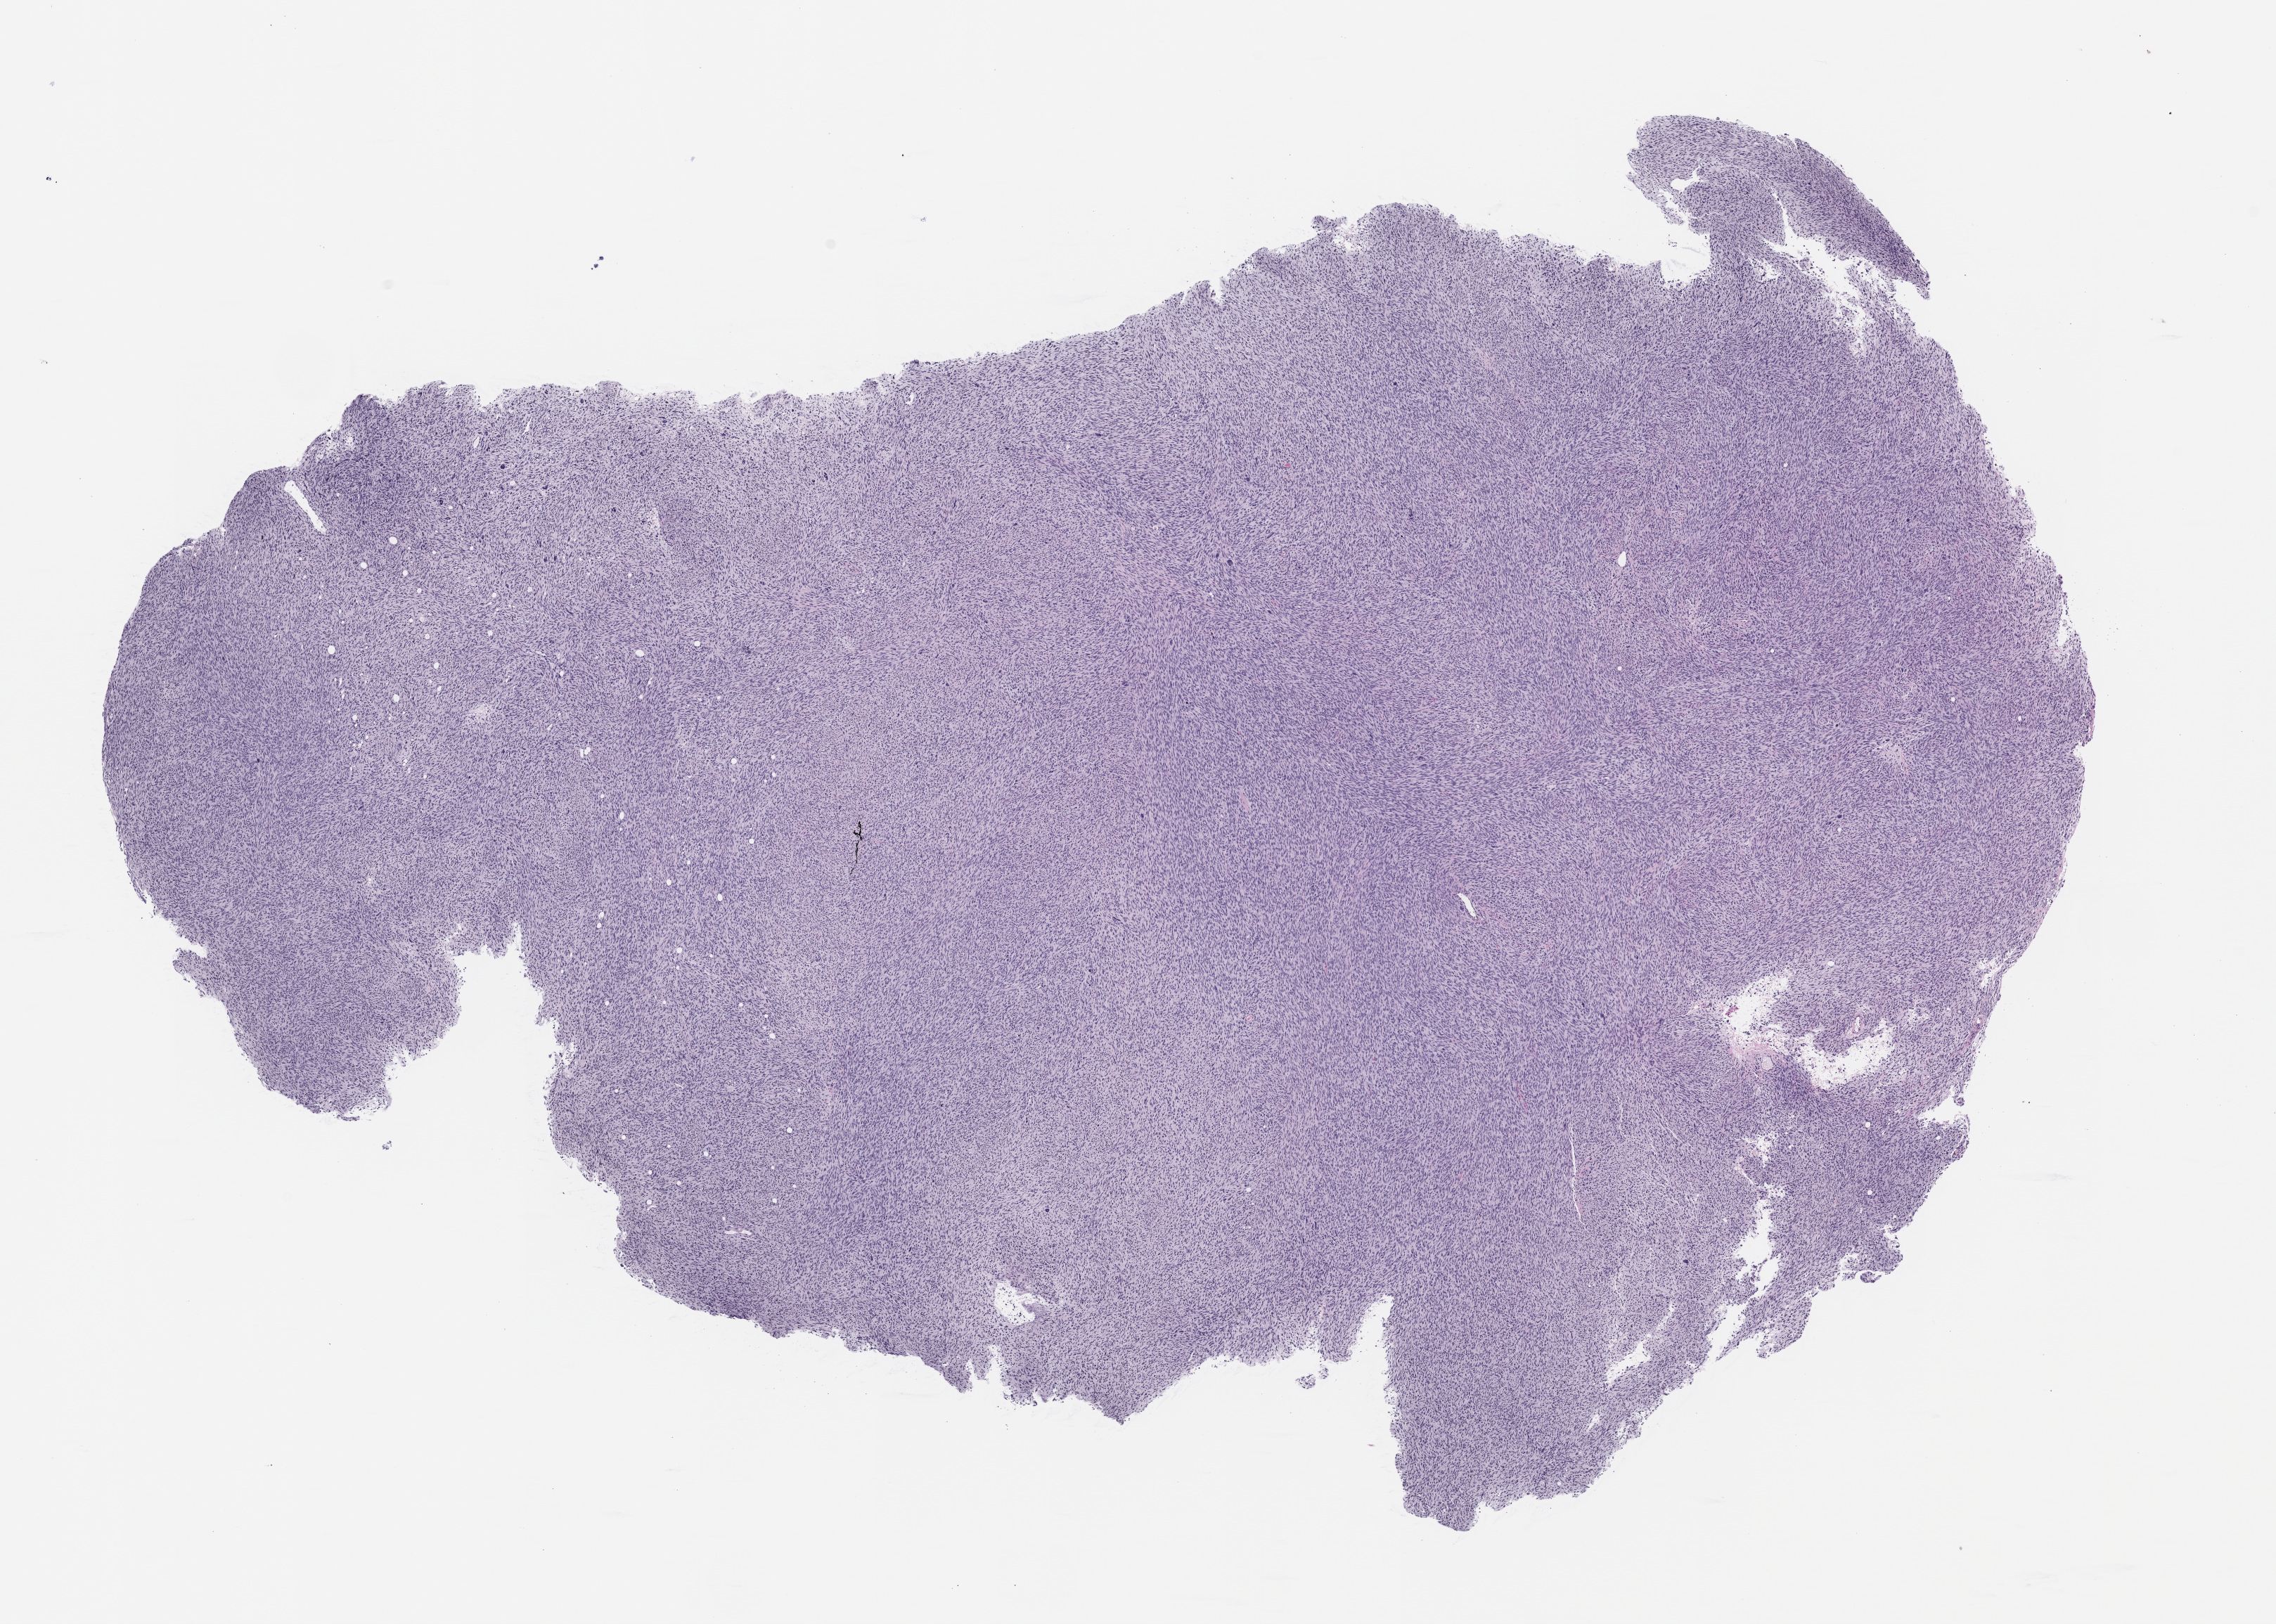
Hematoxylin and eosin (H&E) whole-slide image of a patient-derived xenograft (PDX) tumor grown in a mouse, passage 0, a low-resolution overview of the entire scanned area, about 13.0 x 9.3 mm; formalin-fixed, paraffin-embedded (FFPE) tissue; originating tumor site category: peripheral nervous system.
* originating patient diagnosis: Malignant Peripheral Nerve Sheath Tumor